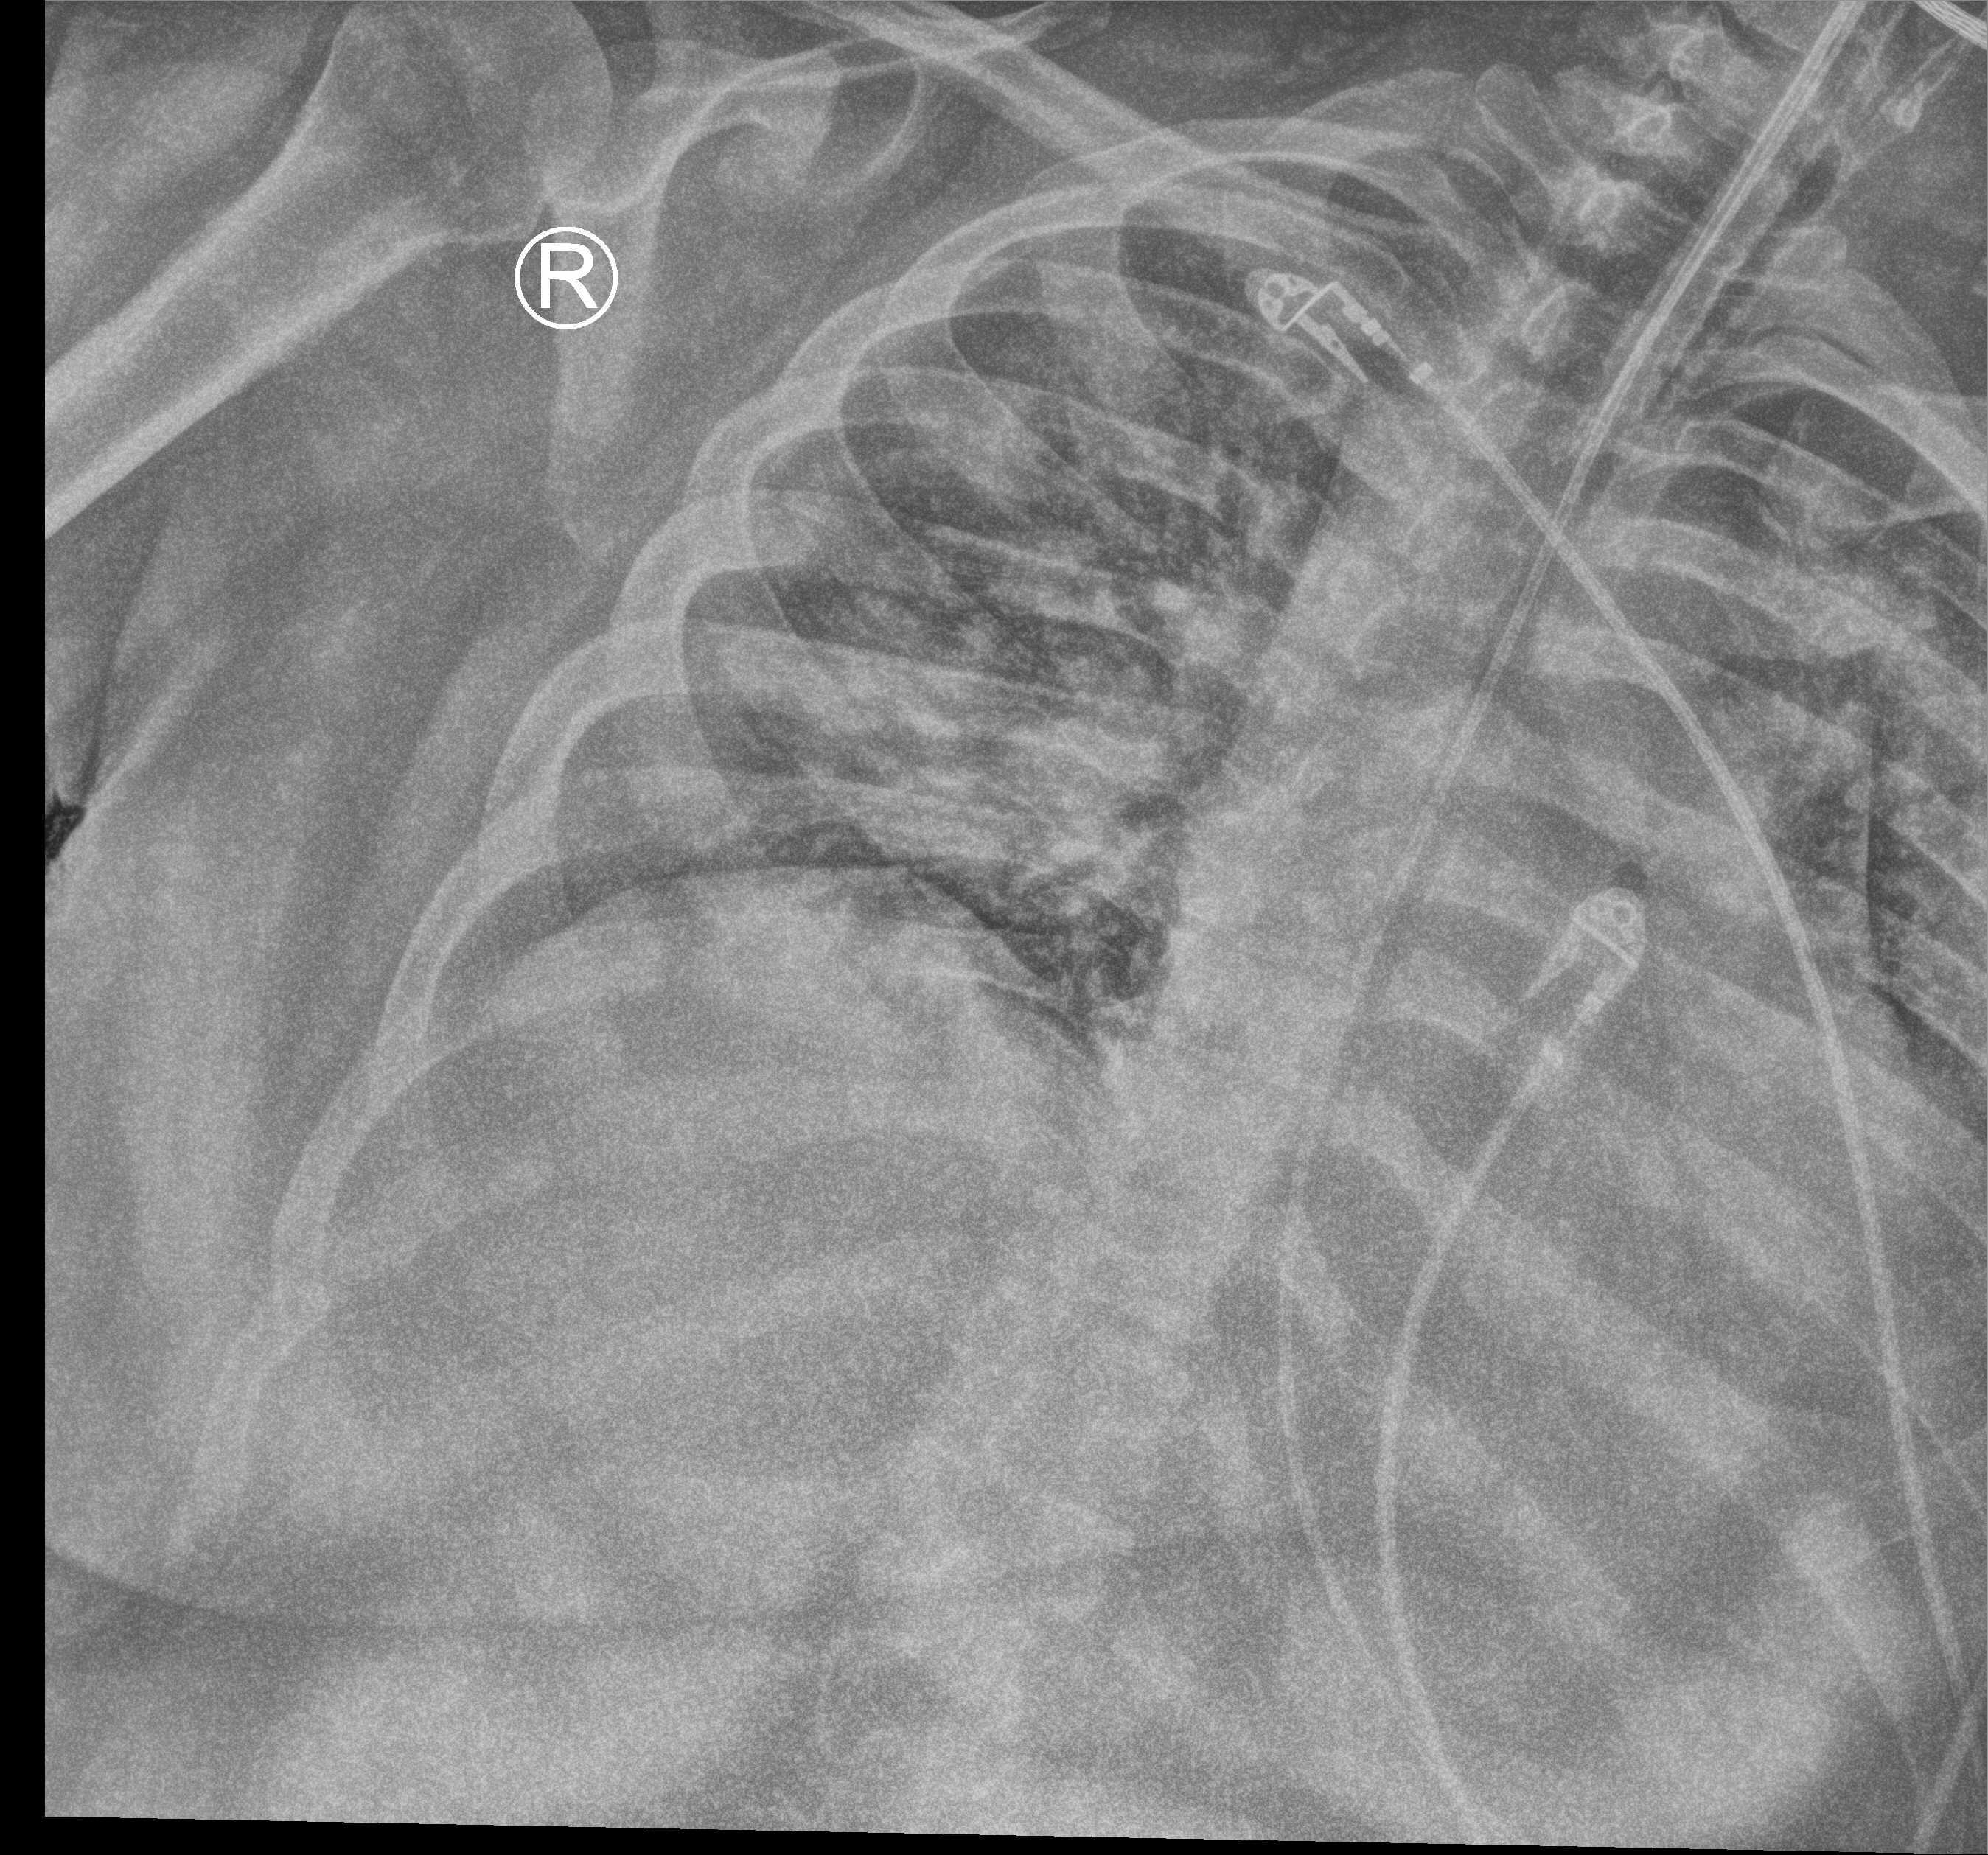
Chest X-ray (portable); anteroposterior (AP) projection. Adult patient hospitalised with COVID-19, age 18–59 years.
Hospital-stay facts (about this admission, not read from this image; timing relative to this image not recorded): mechanically ventilated during this hospital stay: yes.